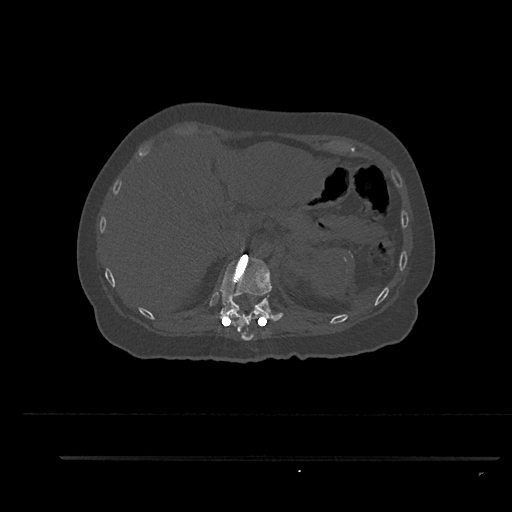
CT including the spine, one axial slice; position 284 of 797 along the scan axis; 120 kVp; bone window (W 1800 / L 400 HU); 0.5 mm slice thickness; 512 × 512 image matrix, field of view 408 × 408 mm. Patient: female, 44 years. From the clinical record (not read from this slice): primary cancer: renal.
Structures marked on this image (semi-automatically segmented with operator editing):
- T11 vertebra: bounding box <232,310,261,341> (left, top, right, bottom; pixels)
- T12 vertebra: <220,246,282,322>